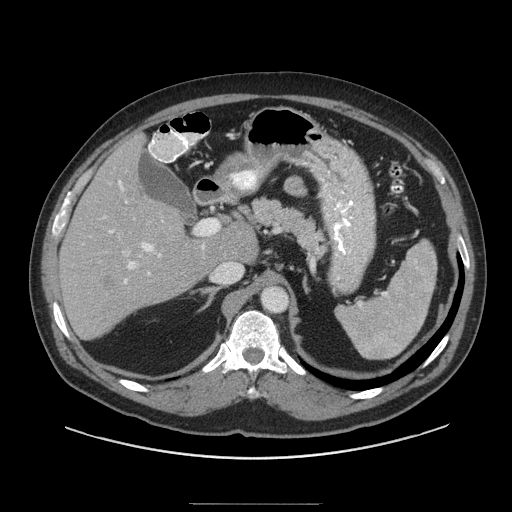
Contrast-enhanced abdominal CT (liver protocol), one axial slice. Position 59 of 91 along the scan axis. 140 kVp. Soft-tissue window (W 400 / L 40 HU). 2.5 mm slice thickness. 512 × 512 image matrix, field of view 440 × 440 mm. From the clinical record (not read from this slice): diagnosis: hepatocellular carcinoma (patient treated with transarterial chemoembolisation; whether this scan precedes or follows treatment is not stated here); TNM stage (as recorded): Stage-I; Child-Pugh class: A; tumour size: 4 cm.
Outlined on this slice (semi-automatic segmentation, software-assisted and operator-edited):
- liver parenchyma outside the tumour (the mass and vessels are separate outlines, so this box may not span the whole liver): box from (x=58, y=132) to (x=256, y=338) px
- mass: (x=97, y=268)–(x=119, y=295)
- liver vessels: (x=104, y=180)–(x=205, y=283)